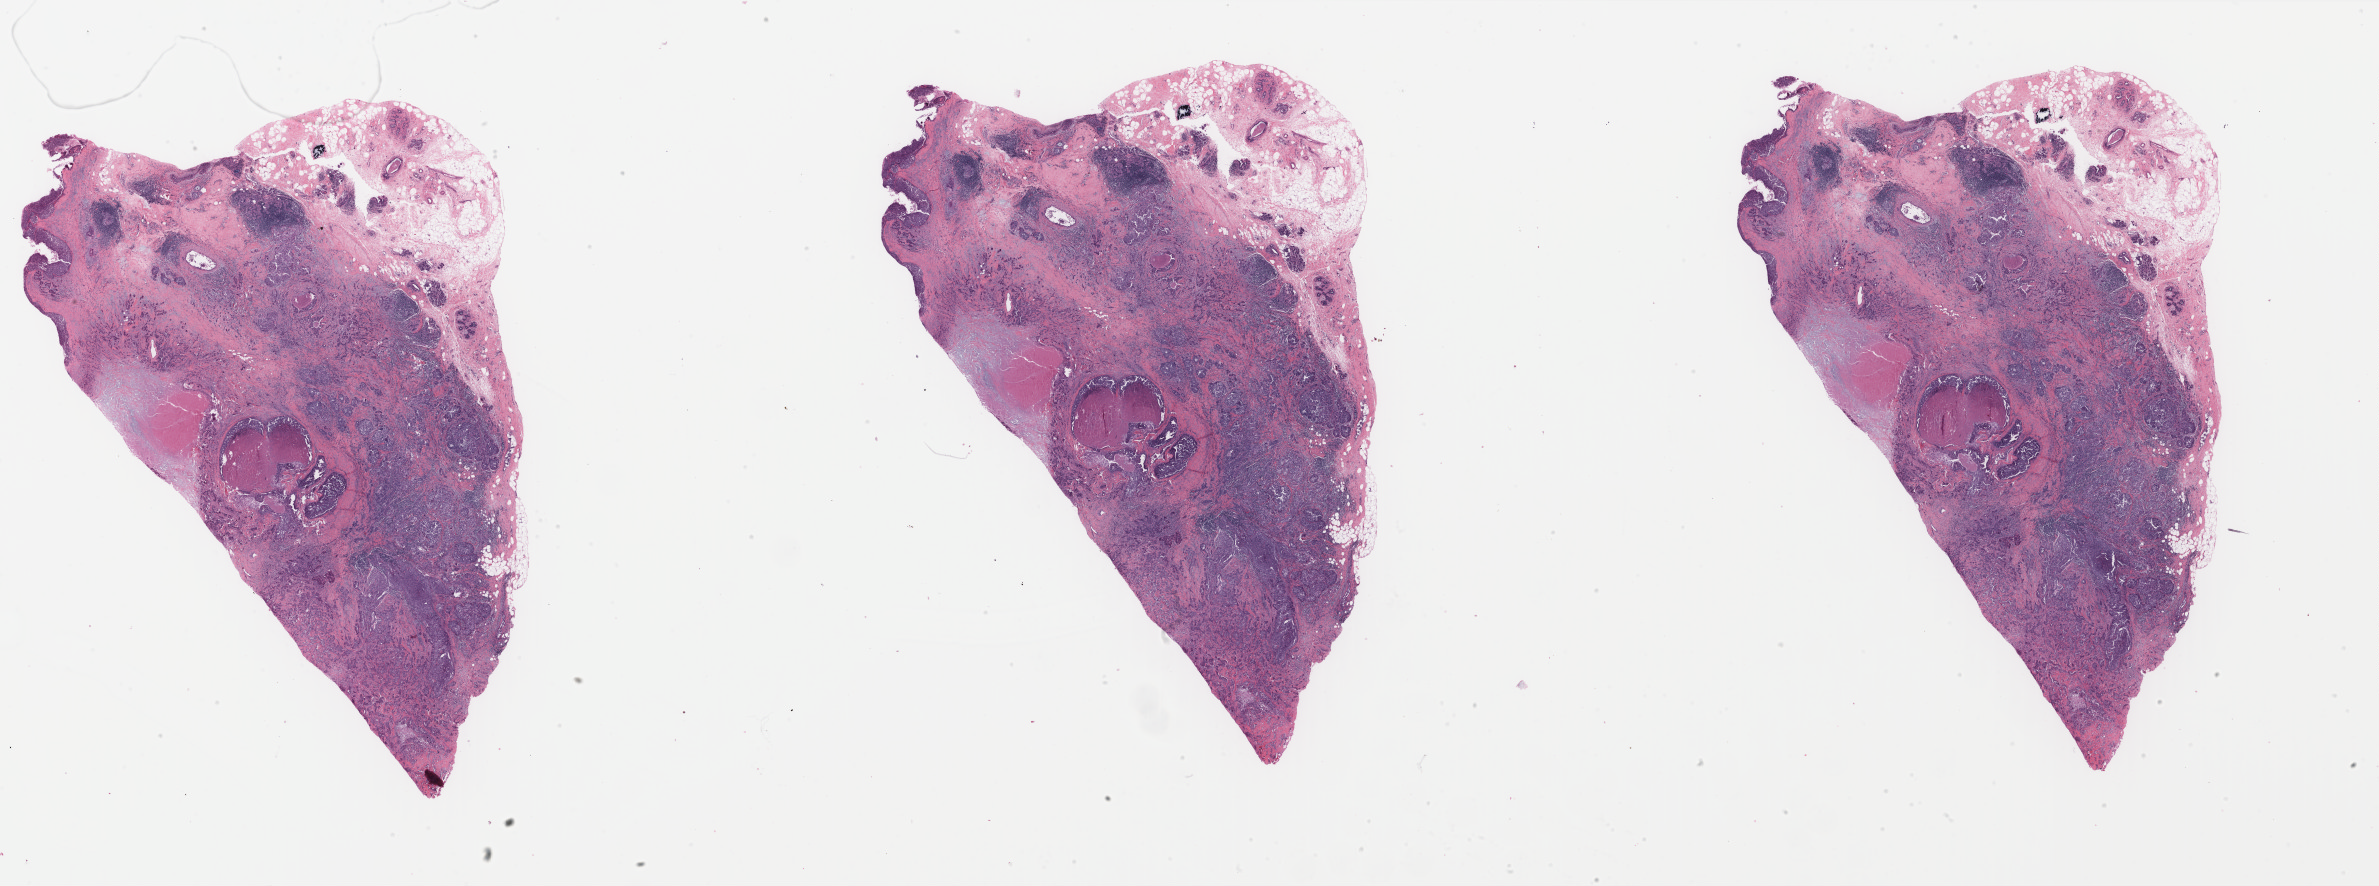
Hematoxylin and eosin (H&E) stained whole-slide image, a low-resolution overview of the entire scanned area, about 37.8 x 14.1 mm (from a 40x scan). Formalin-fixed paraffin-embedded (FFPE) diagnostic section. Primary tumour sample from the breast. Patient: female, age at initial diagnosis 45 years.
* AJCC pathologic stage: IIA
* TNM: T2 N0 (i+) M0
* lymph nodes positive (case pathology): 0 of 20 examined
* pathologic diagnosis: Infiltrating duct carcinoma, NOS
* laterality: right